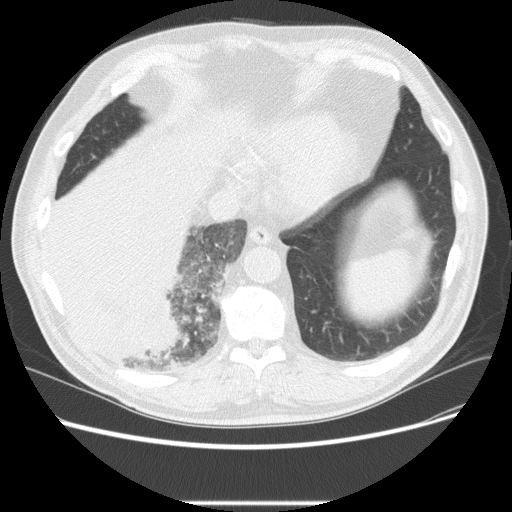
Low-dose screening chest CT, one axial slice; slice 57 of 233 in the series (ordered by position); 120 kVp; lung window (W 1500 / L -600 HU); 2.5 mm slice thickness; 512 × 512 image matrix, field of view 380 × 380 mm.
Annotated regions visible in this slice (manually delineated by an expert):
- lesion 3 (tumor, lower lobe of right lung): bounding box <48,192,182,372> (left, top, right, bottom; pixels)